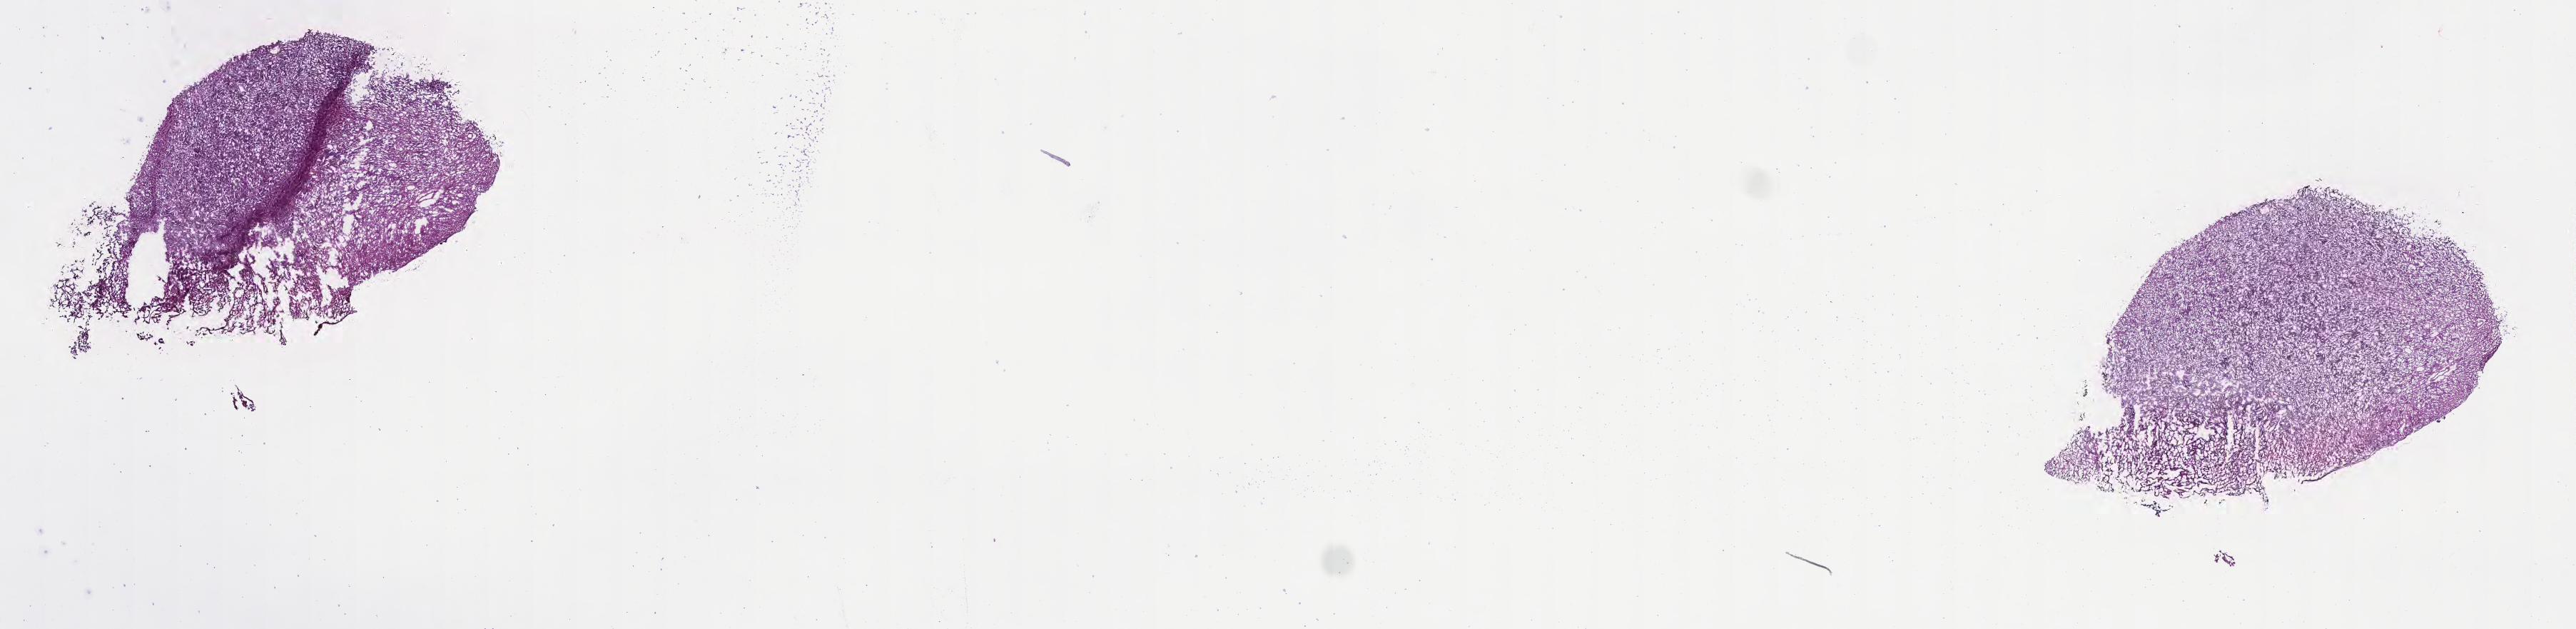
Digitized hematoxylin and eosin (H&E)-stained section of tumor tissue from the brain, a low-resolution overview of the entire scanned area, about 29.2 x 7.1 mm; frozen section (OCT-embedded). Male patient, age 727 days (about 2.0 years).
Diagnosis: Tumor cells, malignant.